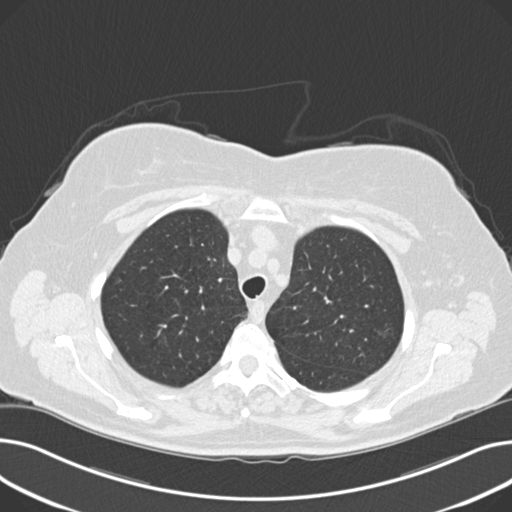
Axial slice from a low-dose chest CT screening exam, third screening round (two years after baseline), lung window (W 1500 / L -600 HU), 2 mm slice thickness, standard (soft-tissue) reconstruction kernel (B30f), slice 49 of 203 in the series, 512 × 512 image matrix, field of view 372 × 372 mm. Female, age 60 years at enrolment. Current smoker at enrolment.
Lesion marked by an expert reader, bounding box (x1, y1, x2, y2) in pixels: (366, 318, 404, 355). The screening reader recorded 8 non-calcified nodules or masses ≥4 mm on this exam (right upper lobe, lingula, lingula, right middle lobe, right lower lobe, left lower lobe, left lower lobe, left lower lobe); which of them this box marks is not recorded. Later outcome: lung cancer diagnosed 176 days after this screen — non-small cell carcinoma, left upper lobe, poorly differentiated (G3), stage IB (AJCC 6th edition), 7 mm at pathology.